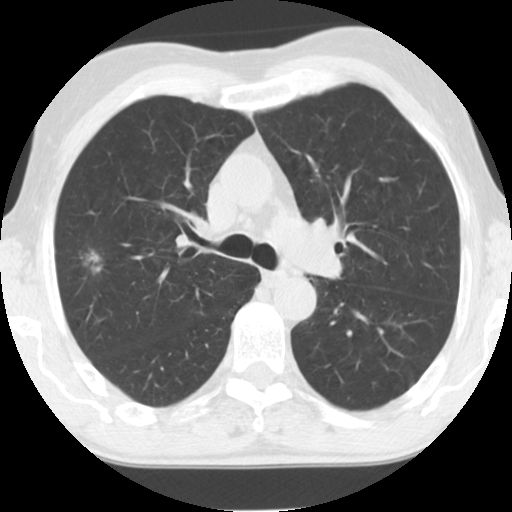
Axial slice from a low-dose chest CT screening exam; second annual screen; lung window (W 1500 / L -600 HU); 2.5 mm slice thickness; standard (soft-tissue) reconstruction kernel (STANDARD); 512 × 512 image matrix. Male, age 69 years at enrolment. Former smoker at enrolment.
Lesion marked by an expert reader, bounding box (x1, y1, x2, y2) in pixels: (67, 242, 120, 287). The exam's reader record, not a measurement of the box and not confirmed to be the same lesion: non-calcified nodule or mass ≥4 mm, right upper lobe, 12 × 8 mm, spiculated (stellate) margins, soft tissue attenuation, pre-existing on the prior screen: yes; interval growth: yes. Official screen result: positive, other. Lung cancer was diagnosed 196 days after this screen: mucinous adenocarcinoma, right upper lobe, moderately differentiated (G2), stage IA (AJCC 6th edition), 11 mm at pathology.